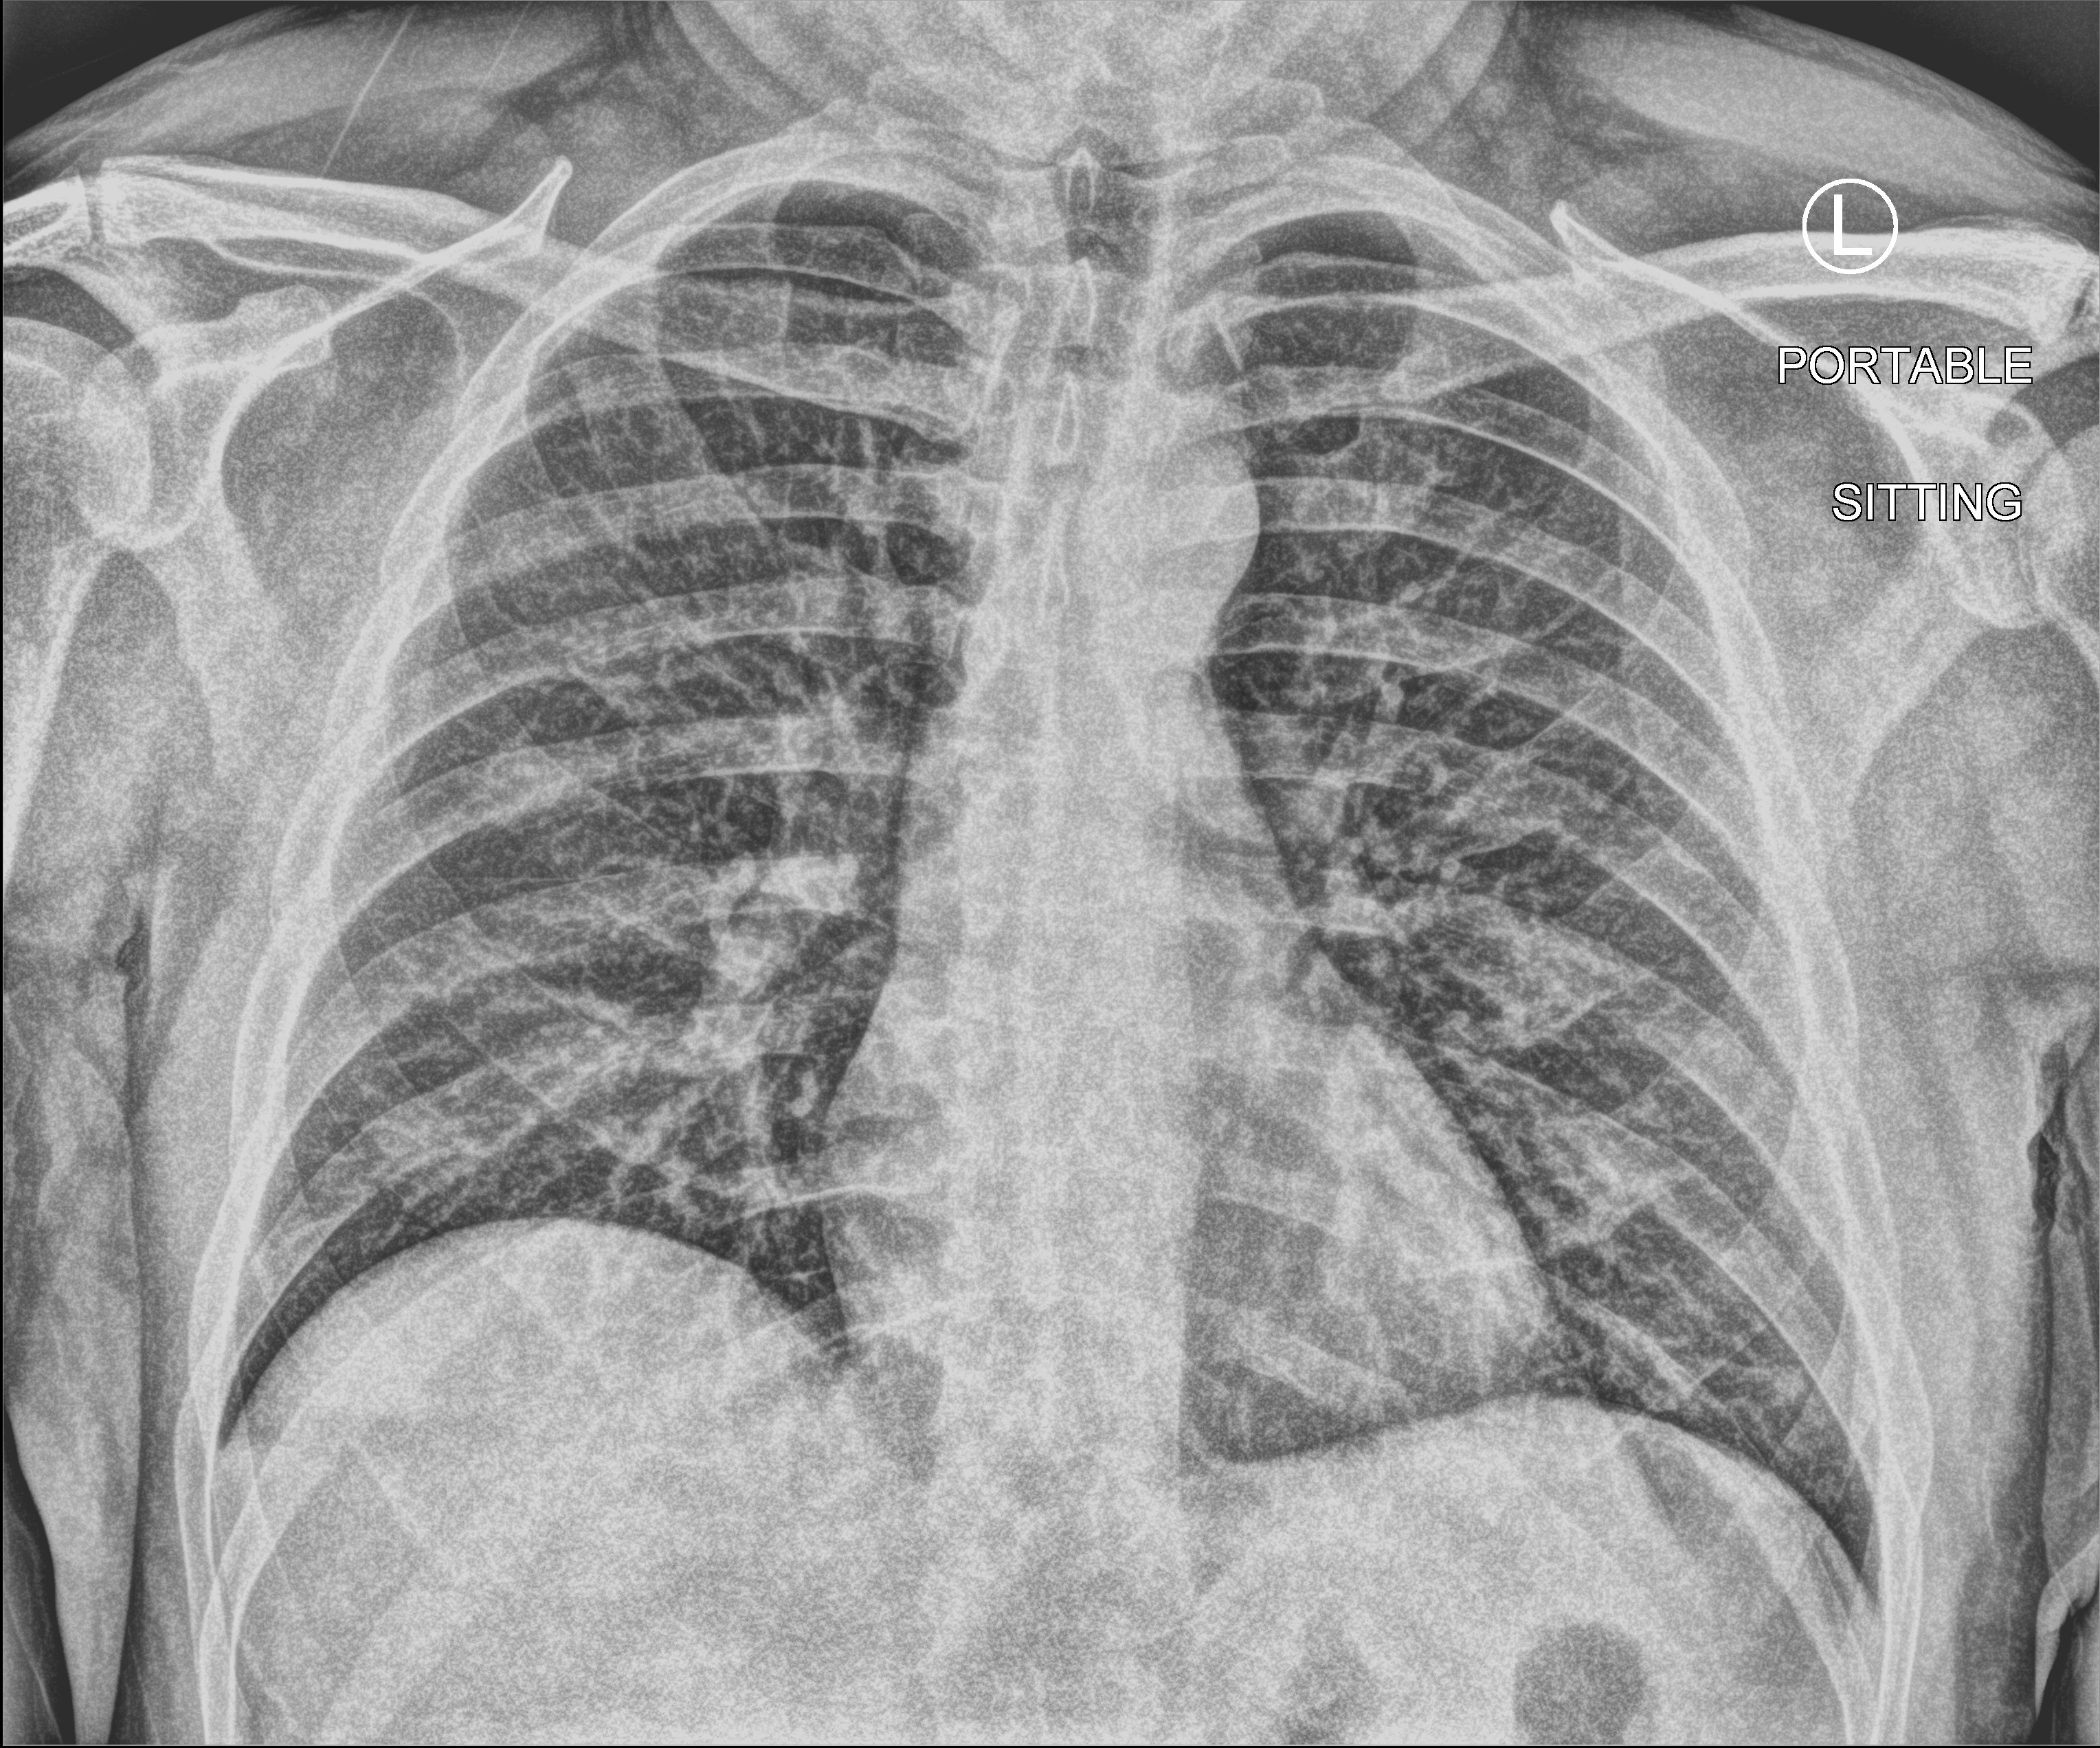
Bedside chest radiograph (computed radiography); anteroposterior (AP) projection. Male patient hospitalised with COVID-19, age 18–59 years.
From the hospital-stay record, not from the radiograph (when in the stay this image was taken is not recorded): mechanically ventilated during this hospital stay: no; admitted to intensive care during this hospital stay: no.